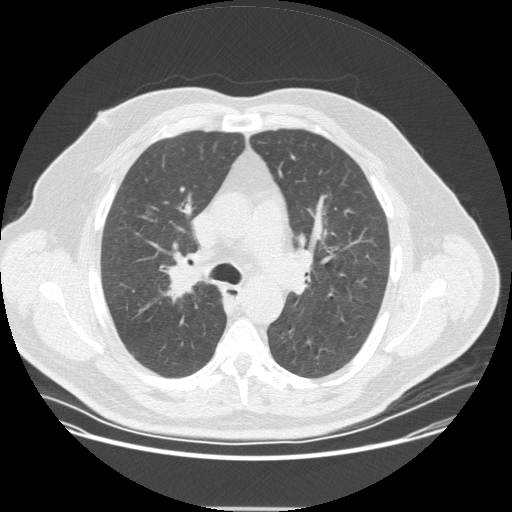
Low-dose screening chest CT, axial slice. Second screening round (one year after baseline). Lung window (W 1500 / L -600 HU). Standard (soft-tissue) reconstruction kernel (STANDARD). Male participant, aged 57 years at enrolment.
- Expert reader's lesion annotation, bounding box [x1, y1, x2, y2] px = [151, 252, 211, 308].
- Screening reader's record for this exam (one nodule recorded; not confirmed to be the boxed lesion): non-calcified nodule or mass ≥4 mm, right upper lobe, 20 × 16 mm, spiculated (stellate) margins, soft tissue attenuation, pre-existing on the prior screen: no.
- Official screen result: positive, other.
- Lung cancer was diagnosed 35 days after this screen: non-small cell carcinoma, right upper lobe, poorly differentiated (G3), stage IIA (AJCC 6th edition), 25 mm at pathology.